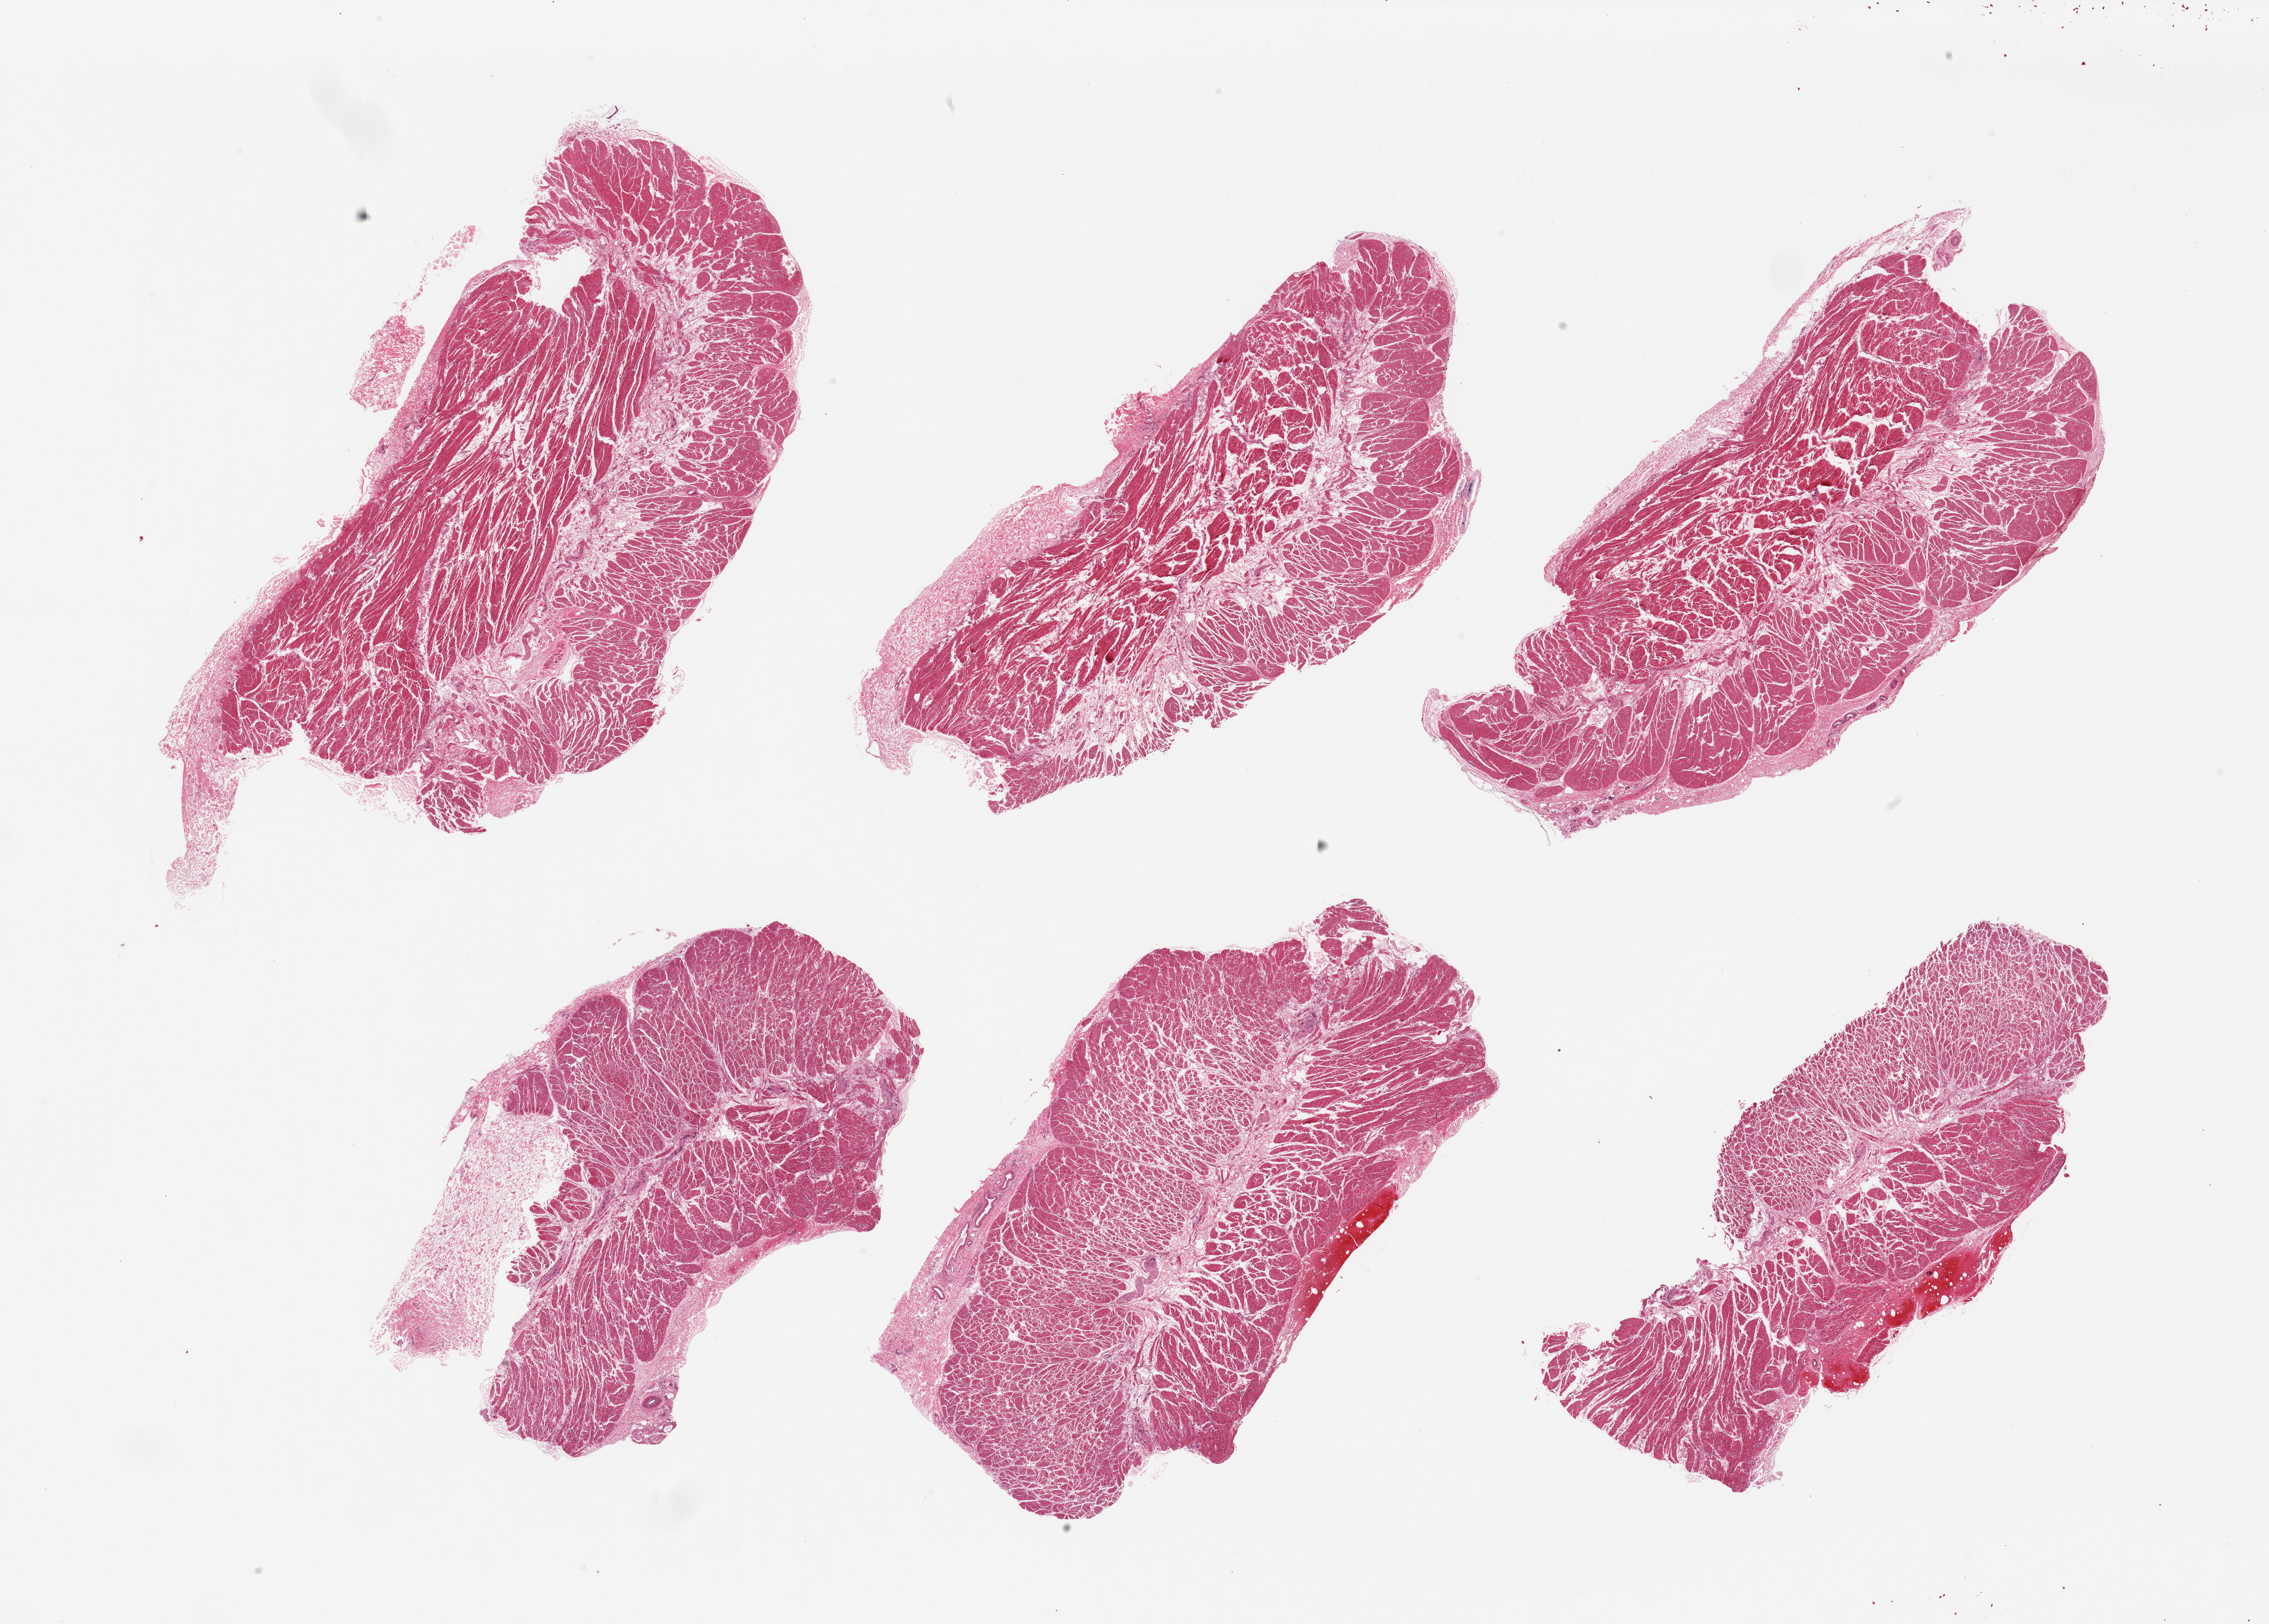
Digitized H&E-stained section, low-resolution overview of the scanned area, about 30.5 x 21.8 mm (acquisition: 20x scan); PAXgene-fixed paraffin-embedded (PFPE) section; sampled site (target tissue): esophageal muscle; tissue donor sample. Donor: female.
Pathologist's review note for this sample: 6 pieces, confirmed target muscularis.